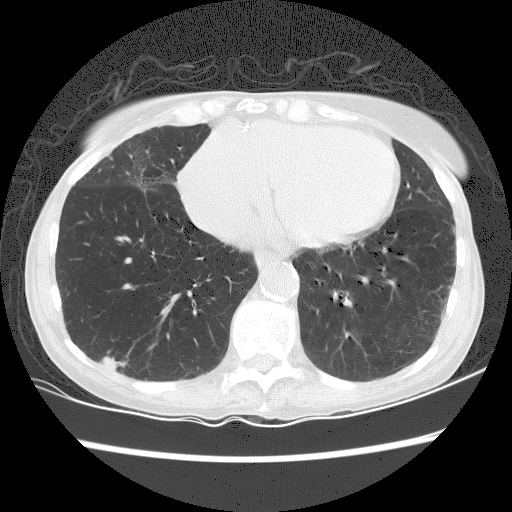
Axial slice from a low-dose chest CT screening exam. Baseline annual screen. Lung window (W 1500 / L -600 HU). 120 kVp. Female participant, aged 70 years at enrolment. Current smoker at enrolment.
Lesion marked by an expert reader, bounding box [x1, y1, x2, y2] px = [87, 345, 138, 386]. The screening reader recorded 2 non-calcified nodules or masses ≥4 mm on this exam (right lower lobe, left lower lobe); which of them this box marks is not recorded. Lung cancer was diagnosed 125 days after this screen: squamous cell carcinoma, NOS, right lower lobe, well differentiated (G1), stage IA (AJCC 6th edition), 25 mm at pathology.